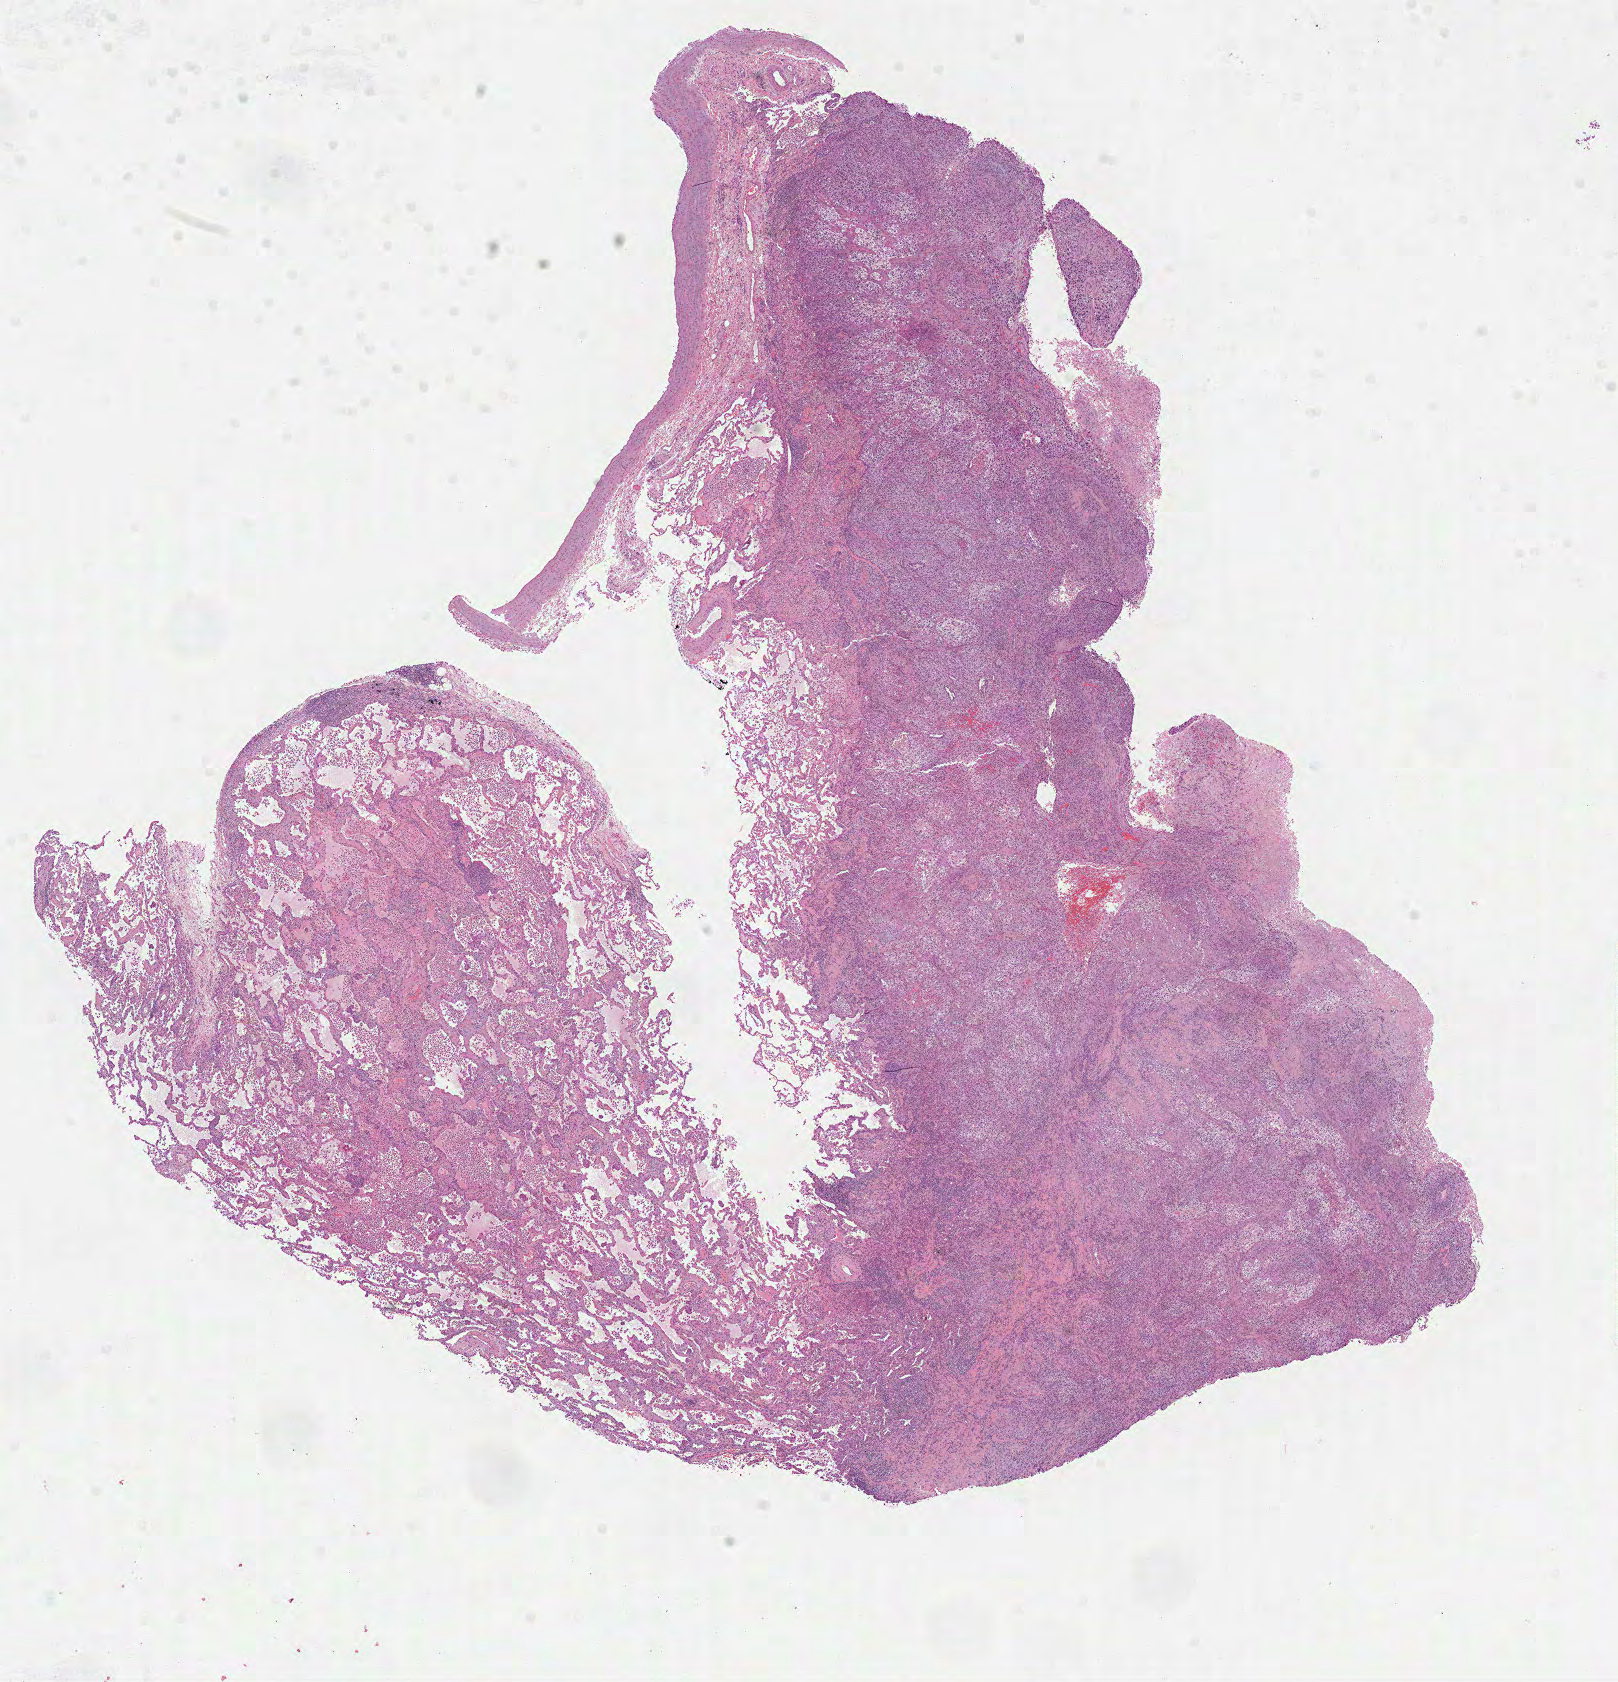
Whole-slide histology image, H&E — low-resolution overview of the scanned area, about 13.1 x 13.6 mm (slide scanned at 40x). Formalin-fixed paraffin-embedded (FFPE) diagnostic section. Sample: primary tumour, lung. Patient: female, age at initial diagnosis 77 years.
- AJCC pathologic stage: IB
- pathologic diagnosis: Squamous cell carcinoma, NOS (upper lobe, lung)
- laterality: right